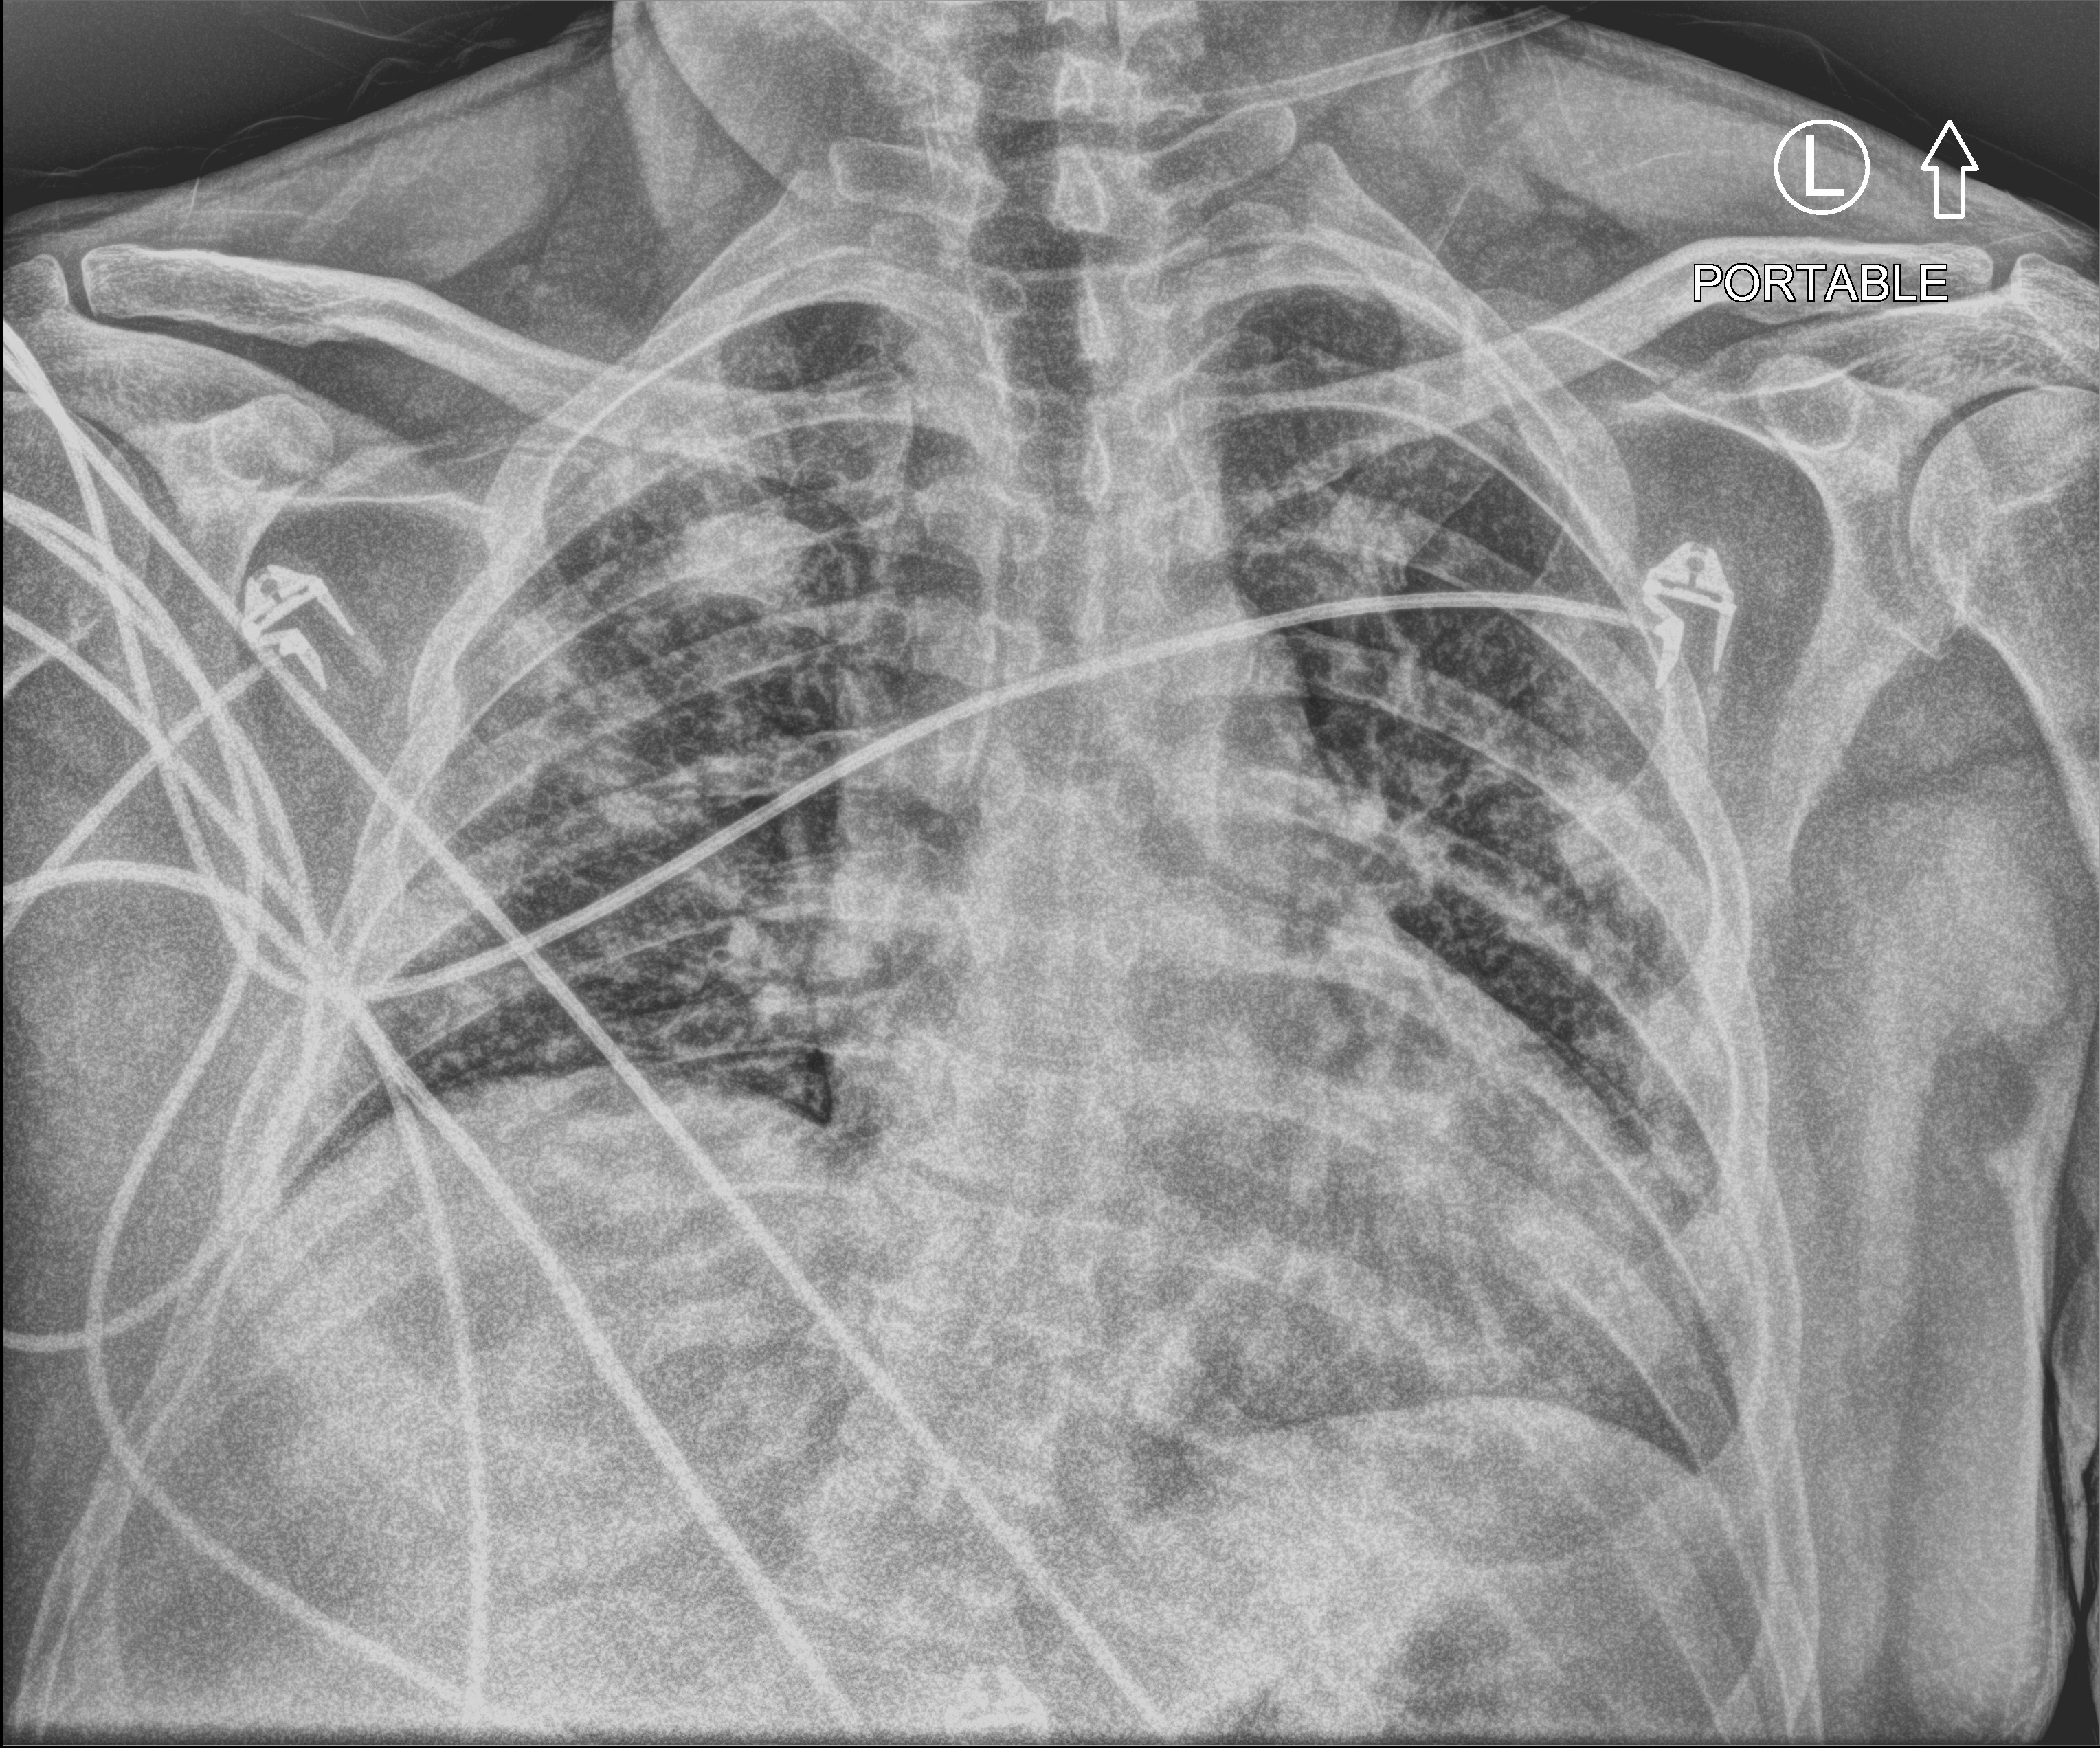
Chest X-ray (portable); anteroposterior (AP) projection. Male patient hospitalised with COVID-19, age 18–59 years.
Admission-level facts for this patient (not findings on this image; timing relative to this image not recorded):
- admitted to intensive care during this hospital stay: no
- mechanically ventilated during this hospital stay: yes